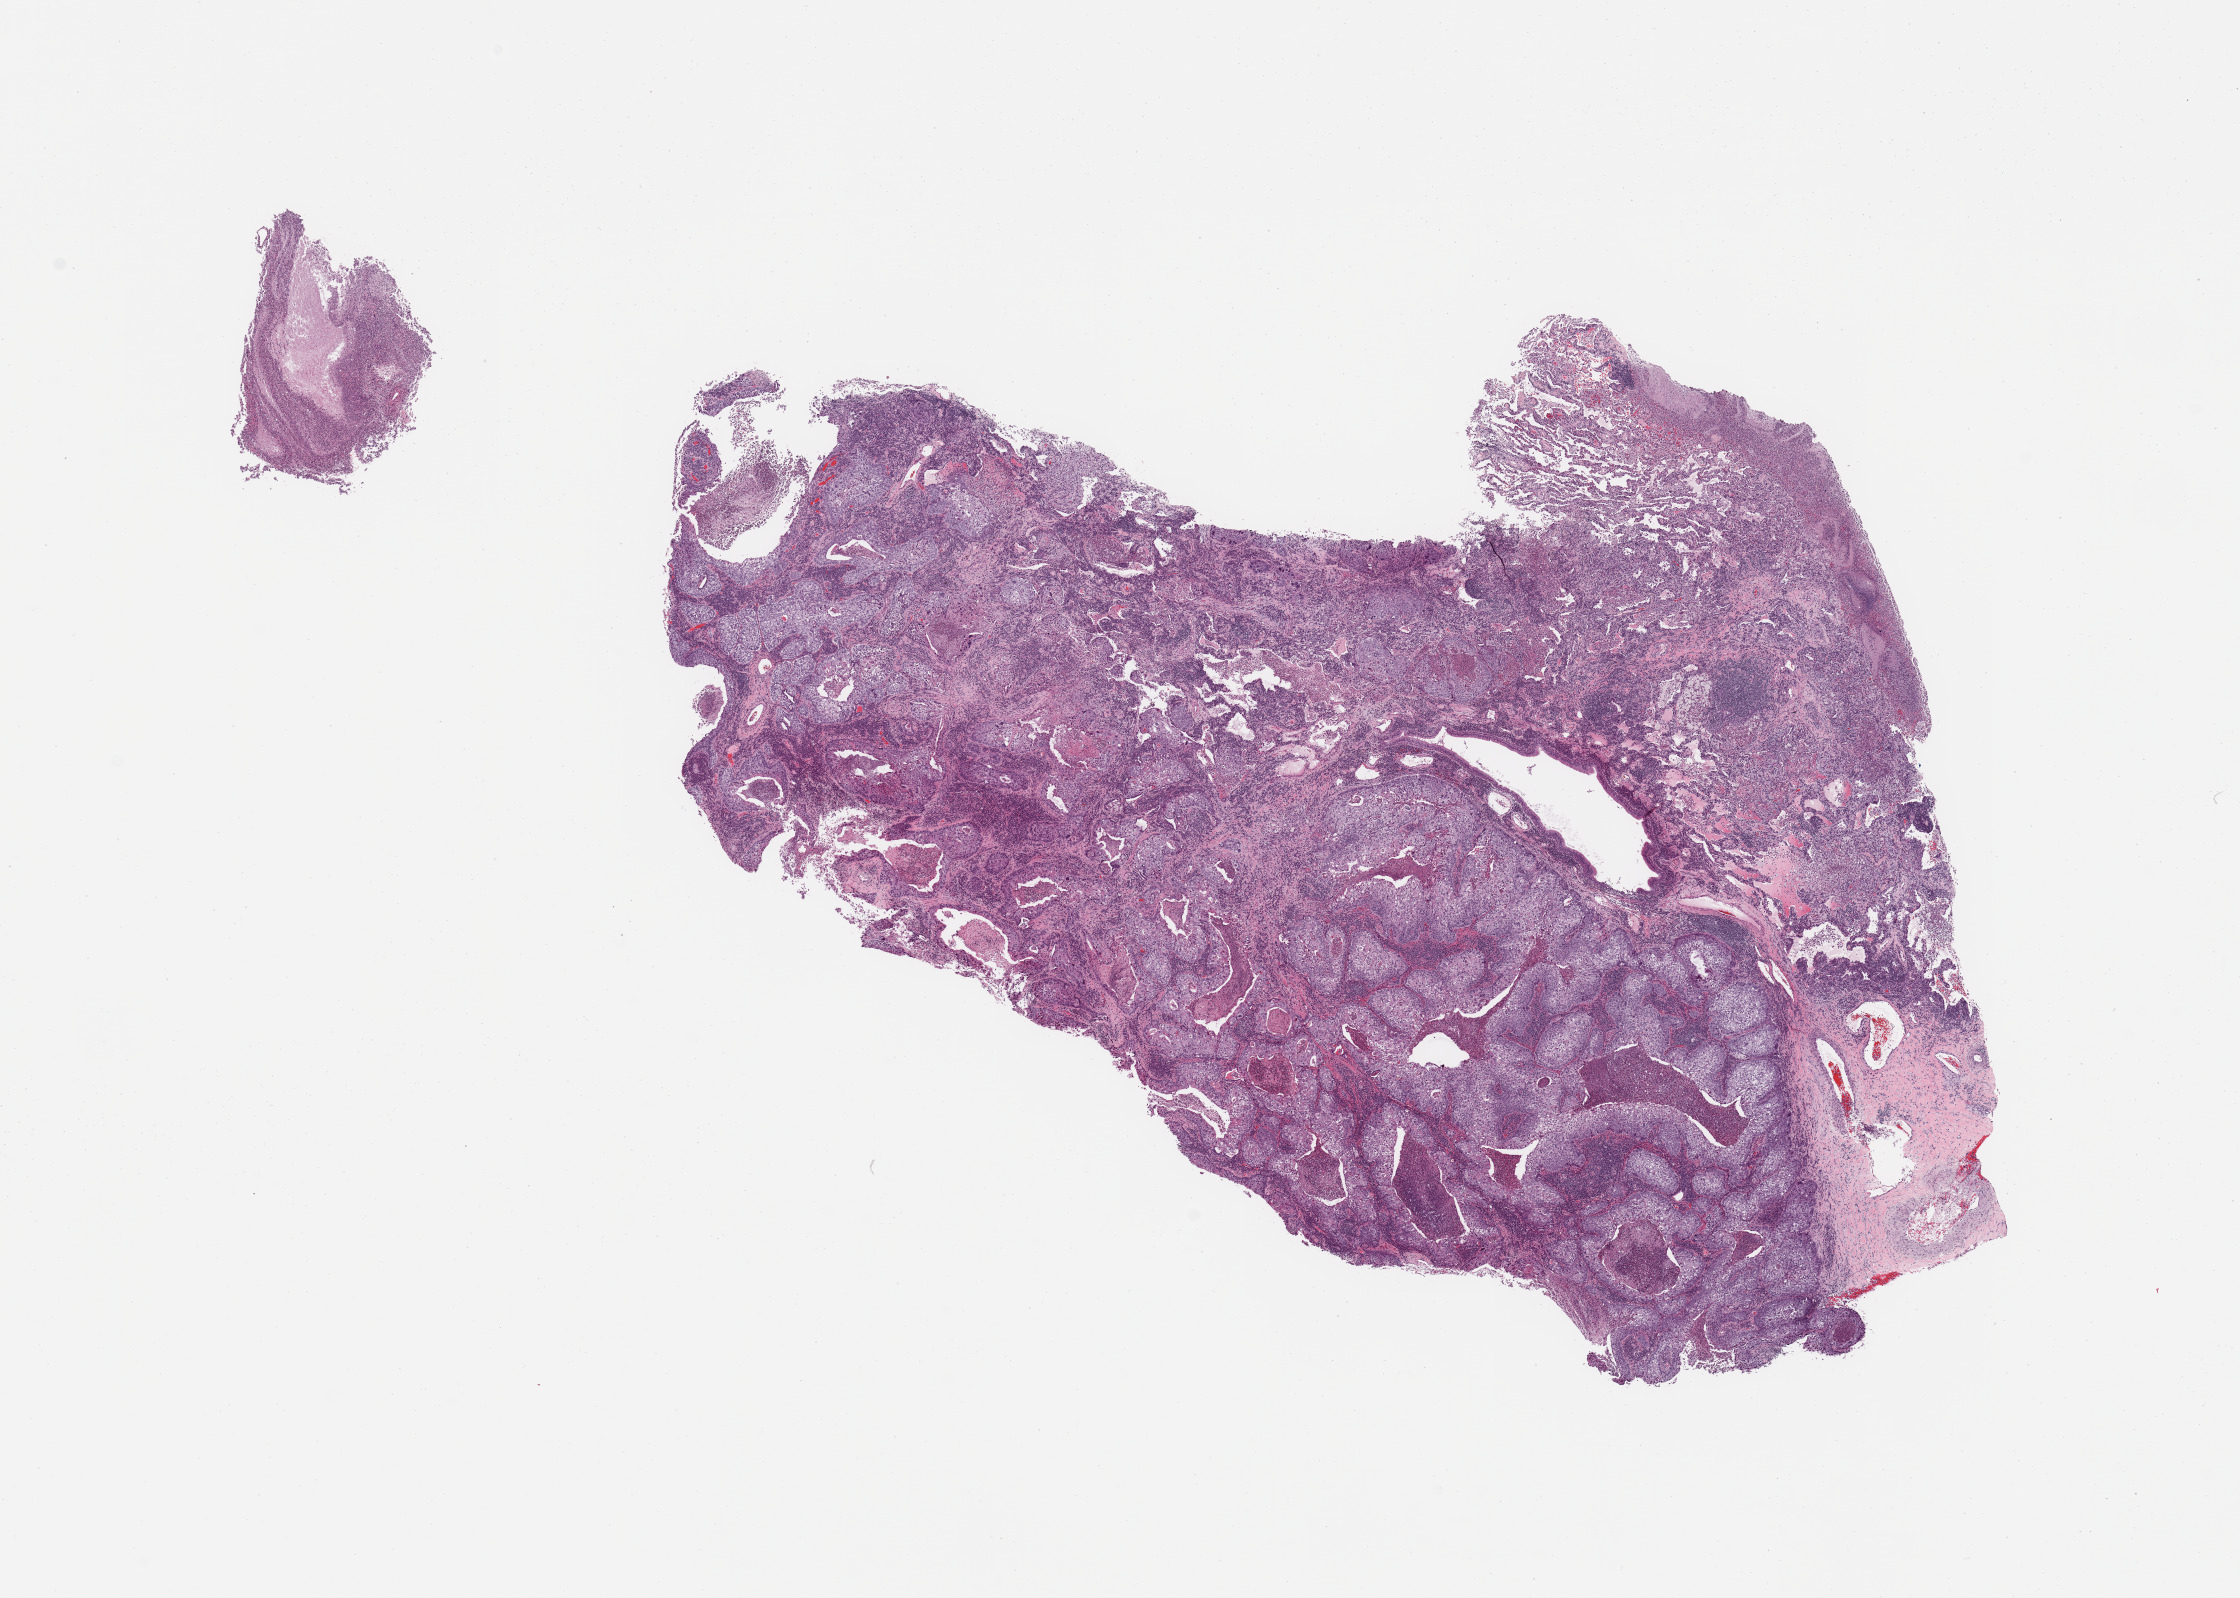
Digitized H&E-stained tissue section (whole slide) — low-resolution overview of the scanned area, about 17.7 x 12.6 mm (from a 20x scan). Lung, tumour tissue. Patient: female, age 64 years. Histologic grade: G3 (poorly differentiated).
Diagnosis: Squamous cell carcinoma, NOS. AJCC pathologic stage: IIA. Primary tumour site (as recorded): left lower lobe.